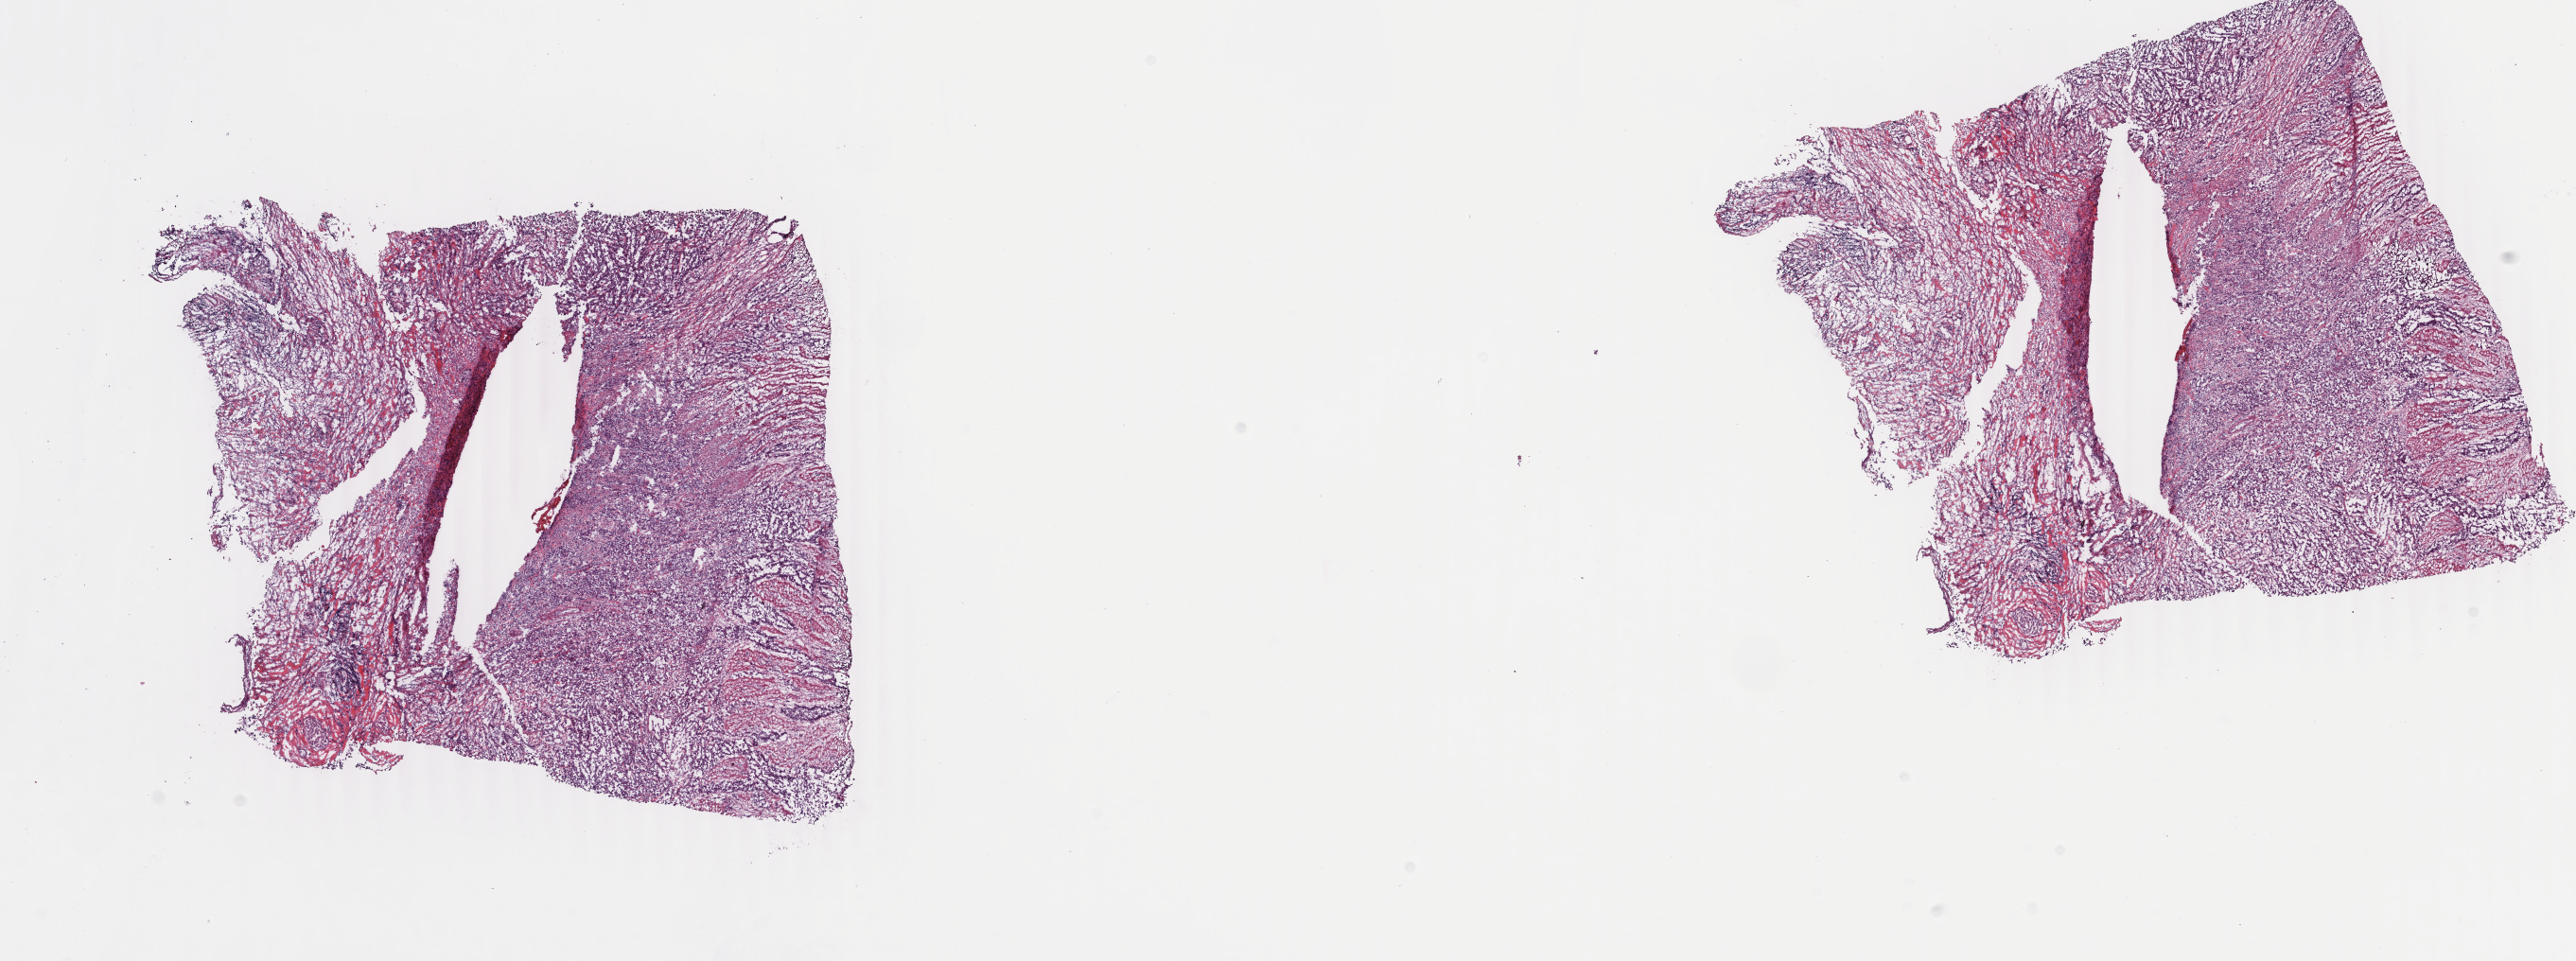
Whole-slide histology image, H&E — whole scanned area (about 21.7 x 8.1 mm, acquisition: 40x scan) shown as a low-resolution overview. Frozen section from the top of the tissue portion. Sample: primary tumour, stomach. Male, age 39 years at initial diagnosis. Histologic grade: G3 (poorly differentiated). Pathologist review of this section (percent, as recorded): tumour cells 53%, tumour nuclei 80%, normal cells 0%, stromal cells 35%, necrosis 12%. Infiltration values recorded for this section: lymphocyte infiltration 6%, monocyte infiltration 0%, neutrophil infiltration 0%.
- histologic diagnosis: Adenocarcinoma, NOS (gastric antrum)
- AJCC pathologic stage: IIIB (7th edition)
- lymph nodes positive (case pathology): 3 of 3 examined